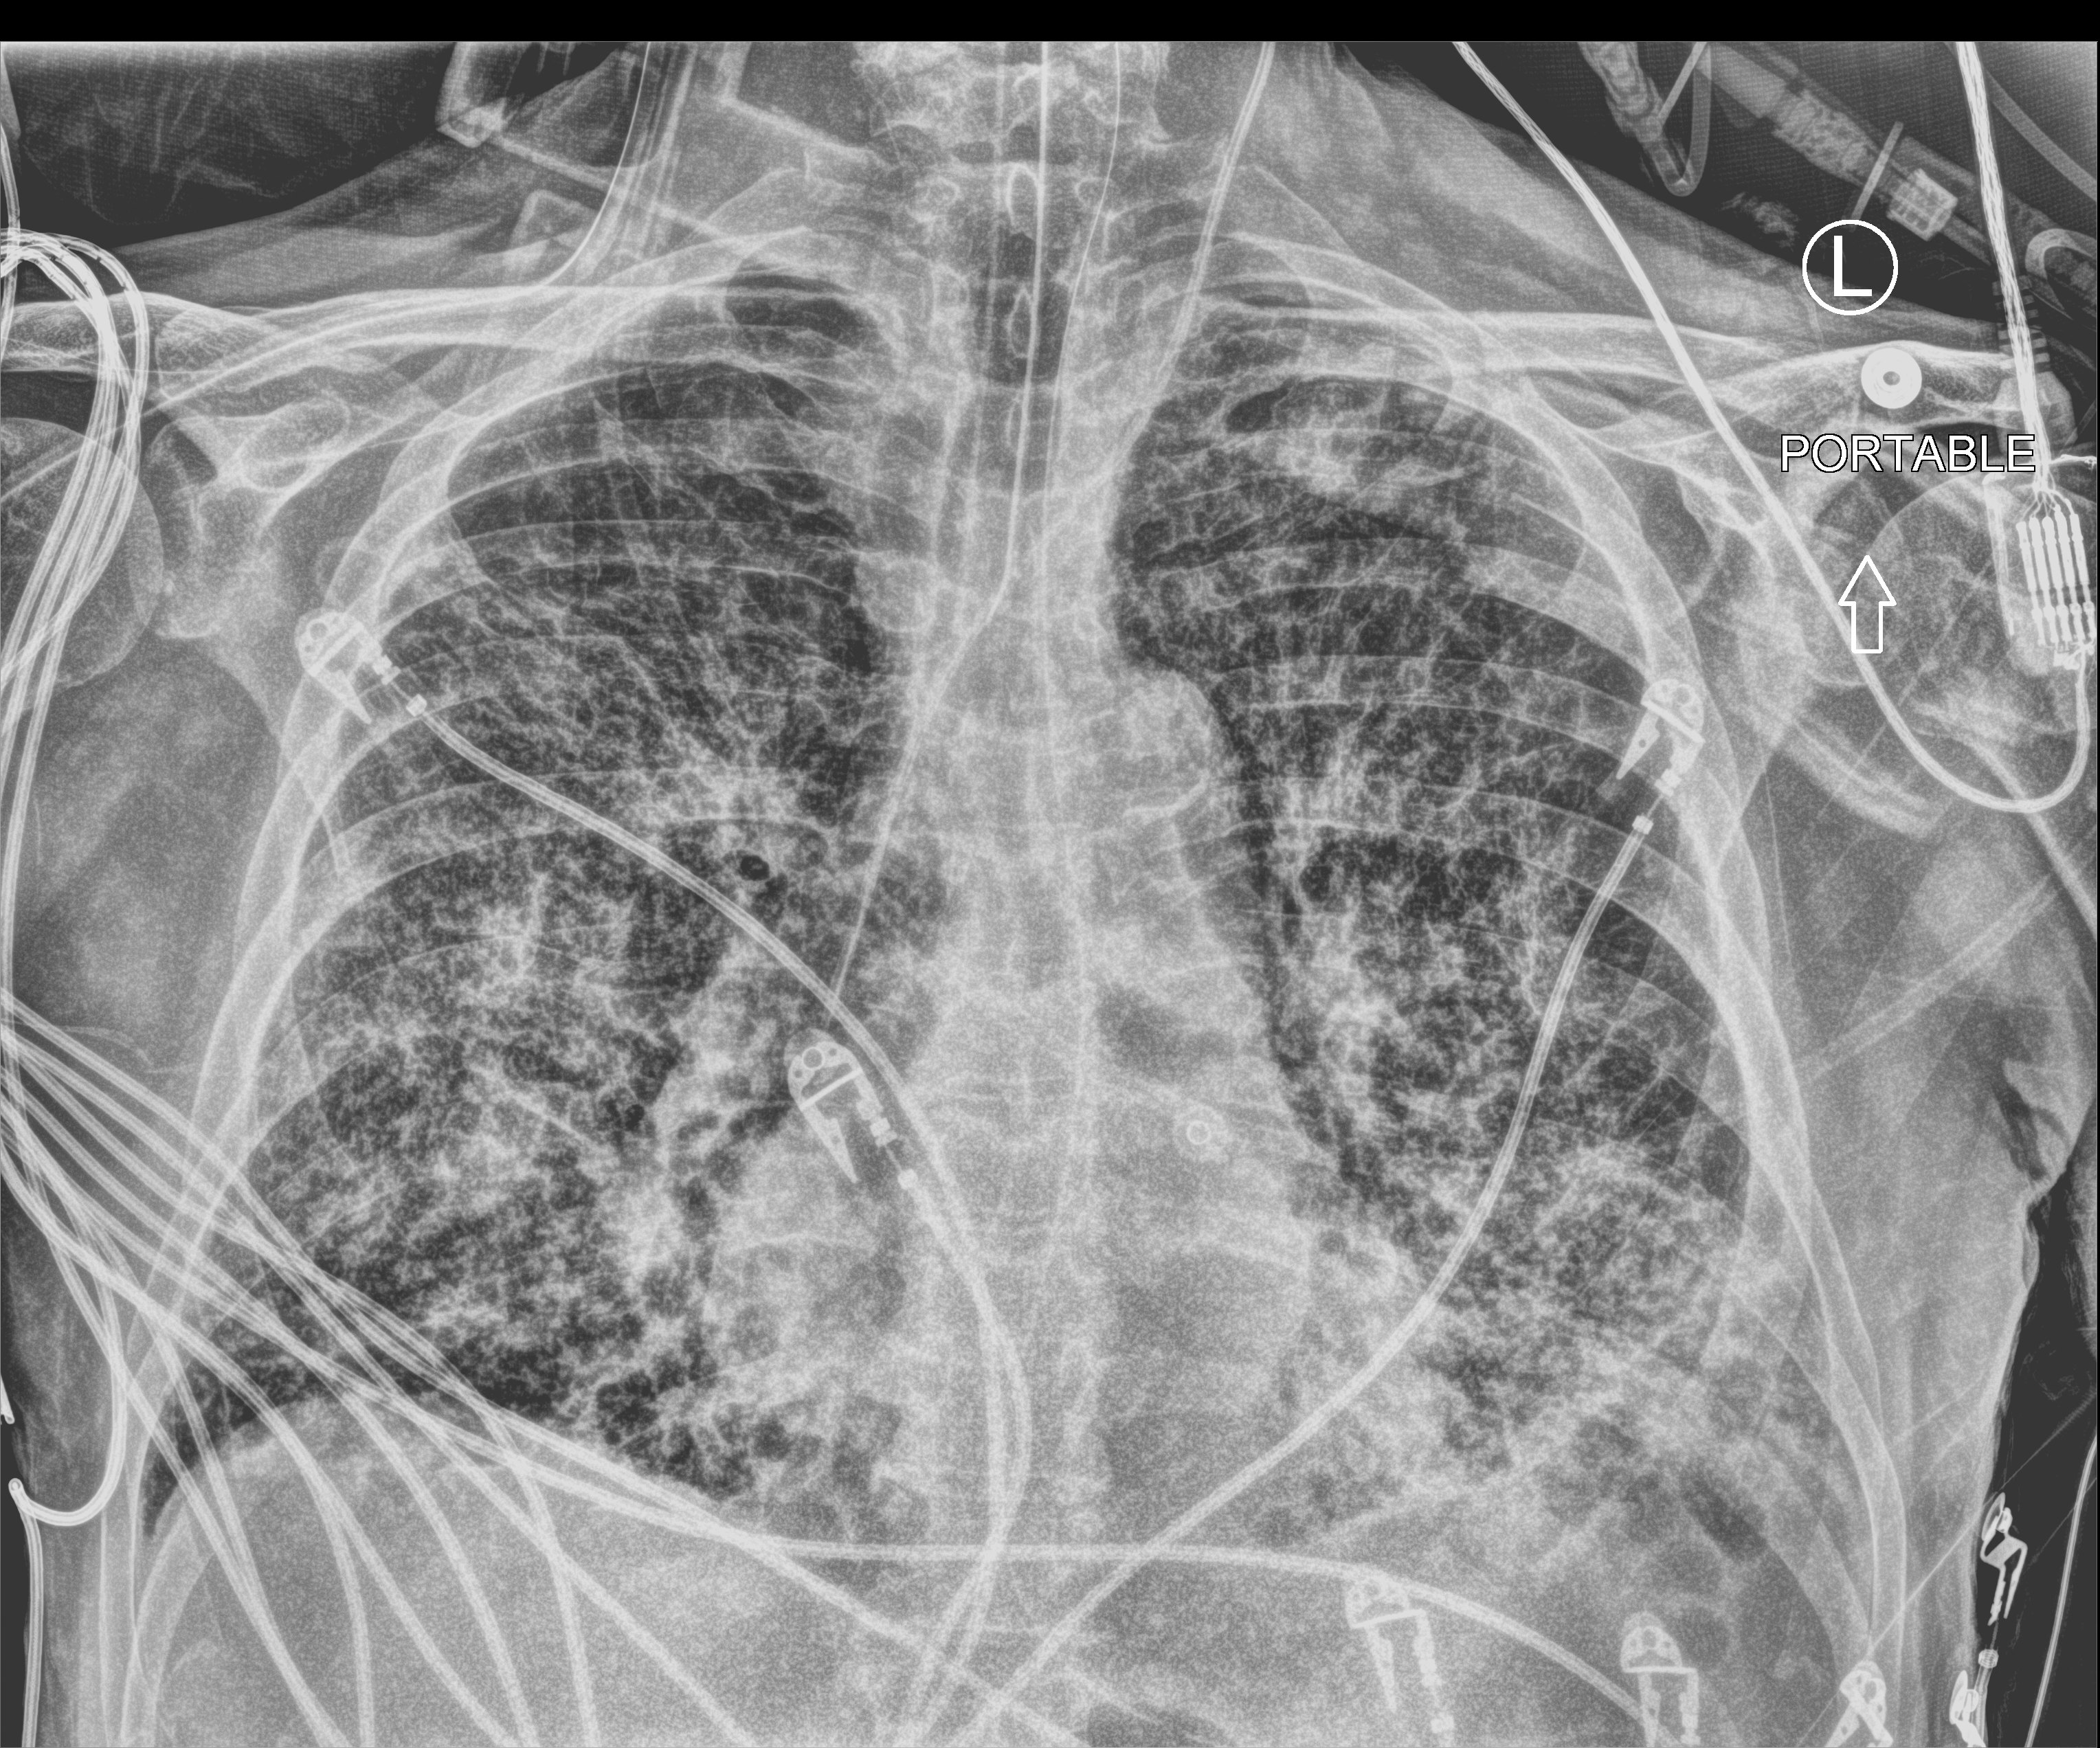
Chest X-ray (portable), anteroposterior (AP) projection. Patient hospitalised with COVID-19; male, aged 75–90 years.
Admission-level facts for this patient (not findings on this image; timing relative to this image not recorded): hypertension (admission record): yes; length of hospital stay: 13 days; chronic kidney disease (admission record): no.